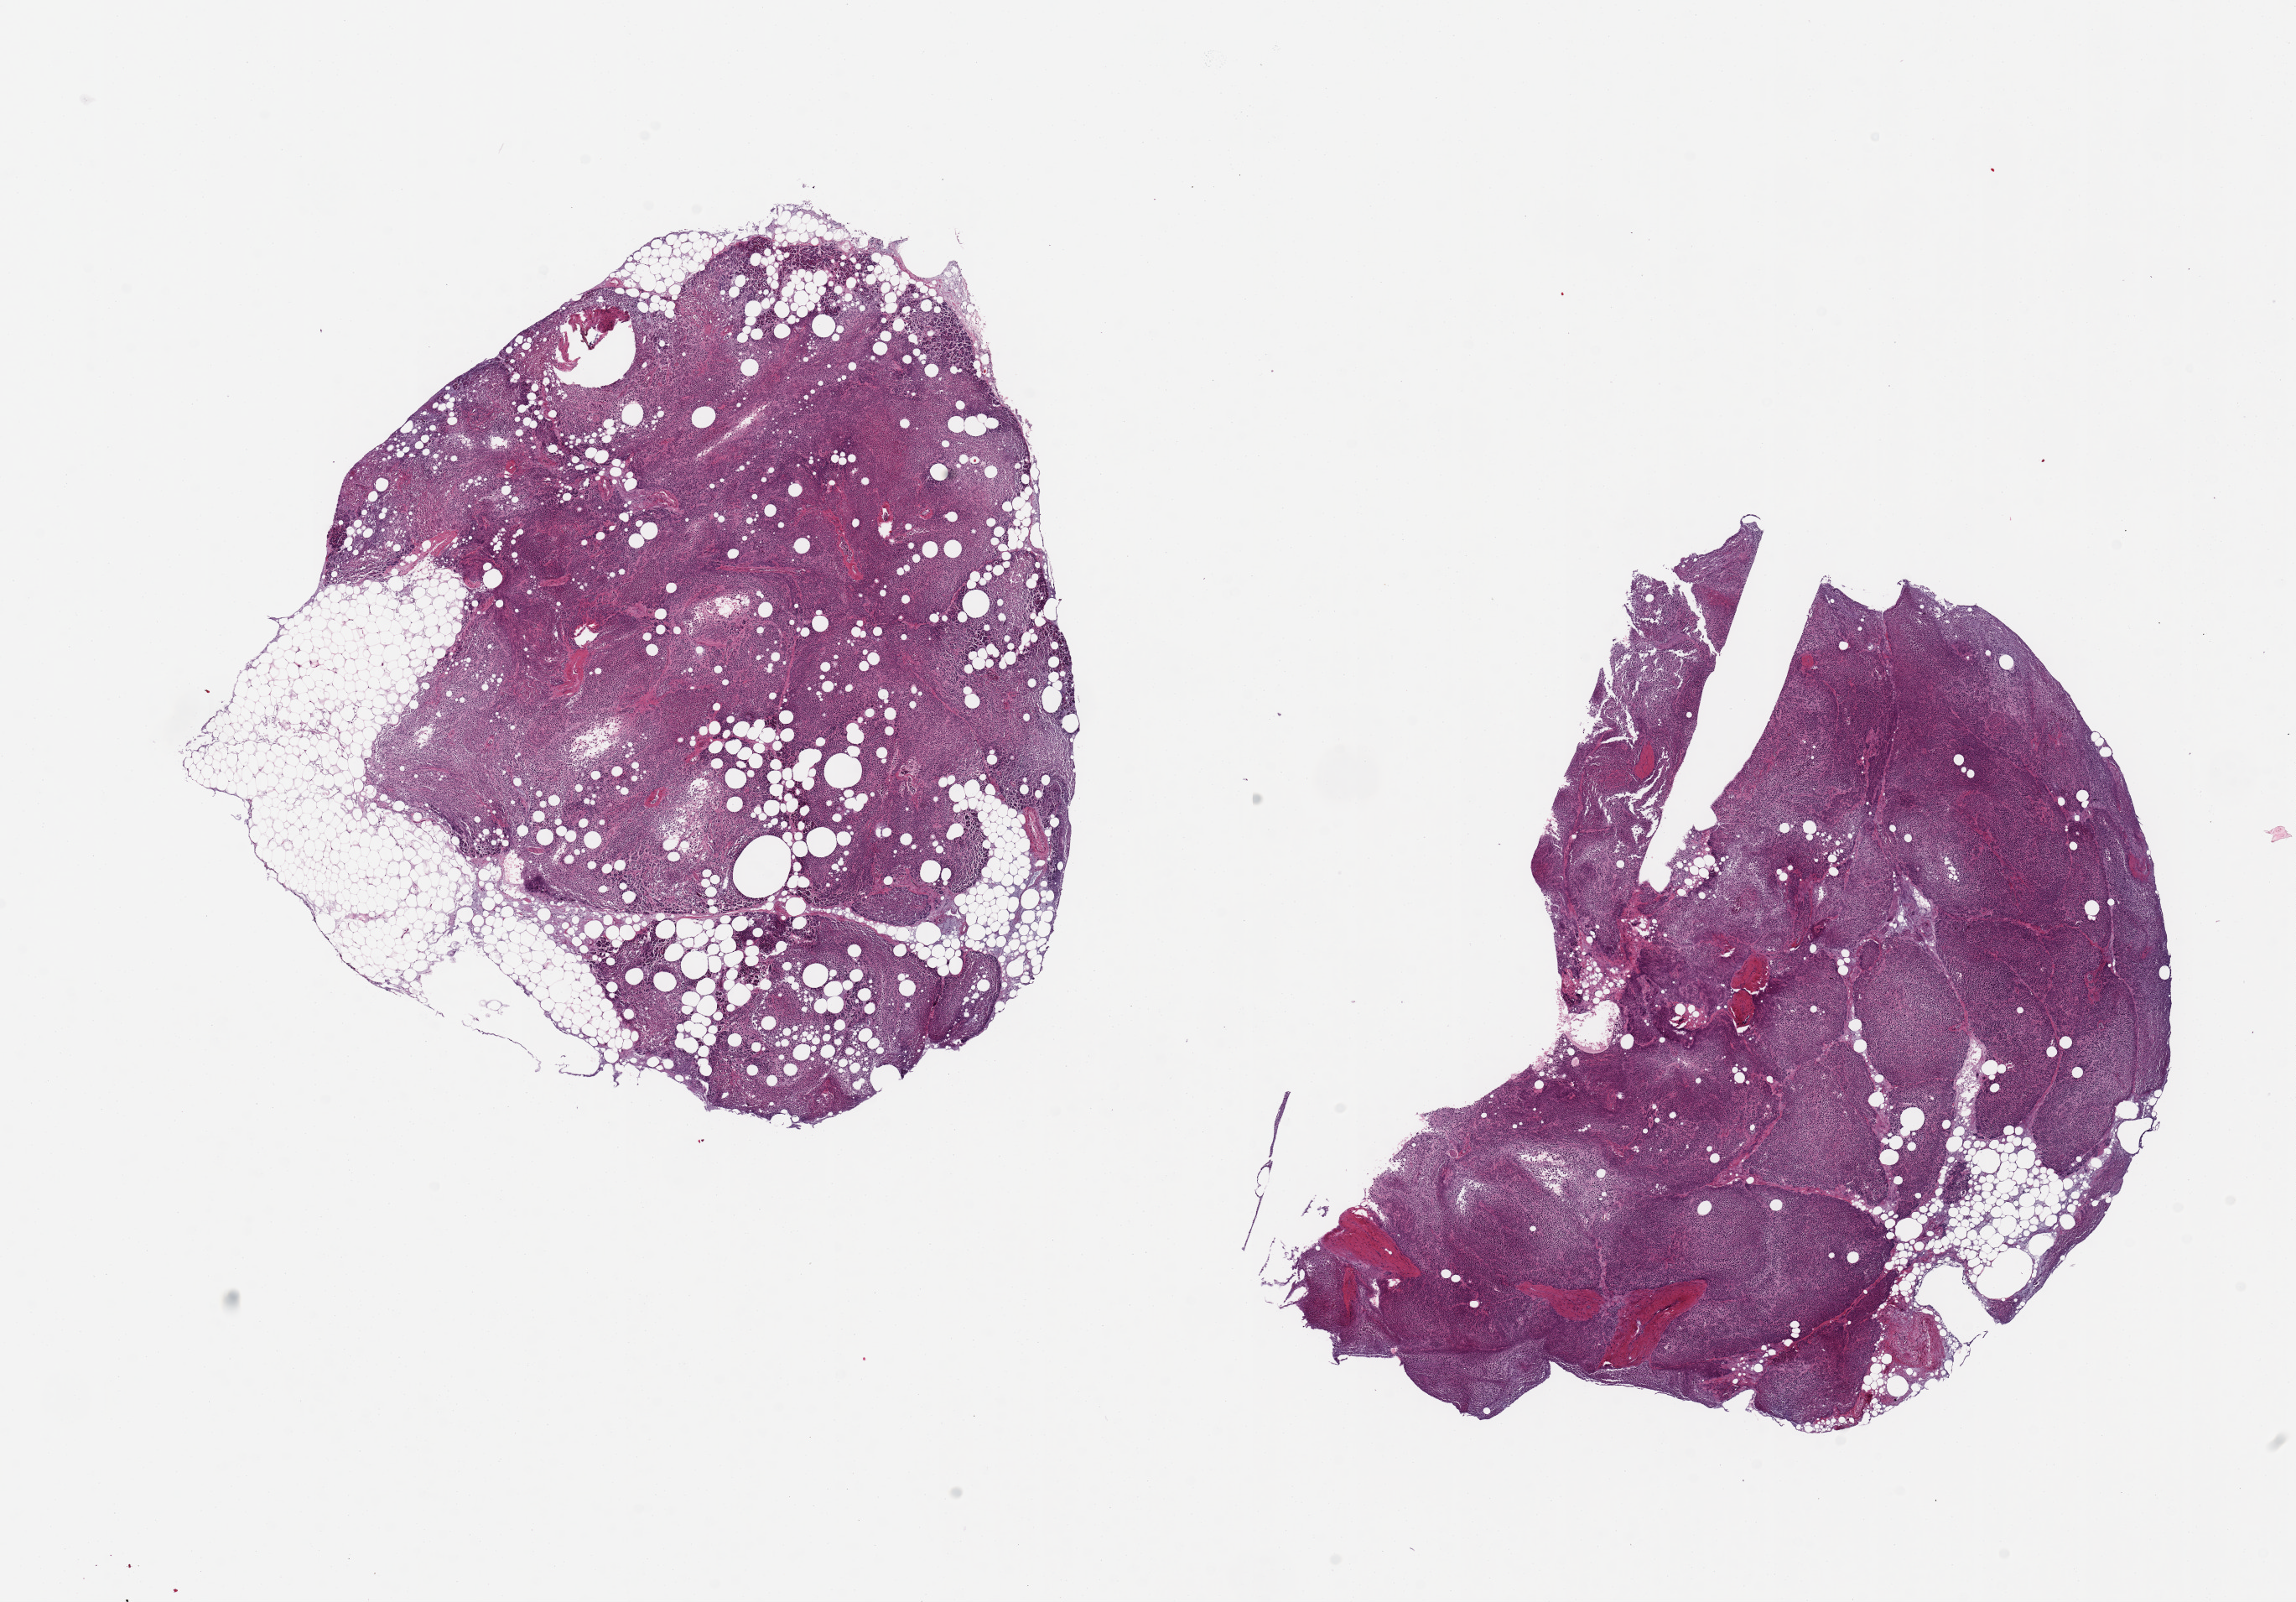
Whole-slide image, H&E stain, a low-resolution overview of the entire scanned area, about 21.7 x 15.1 mm; PAXgene-fixed, paraffin-embedded tissue; section of pancreas (target tissue); donor tissue sample. Donor sex: male.
Pathologist's review note for this sample: 2 pieces, 8.5x7 & 9x7mm; tissue barely recognizable; 10-20% adipose.